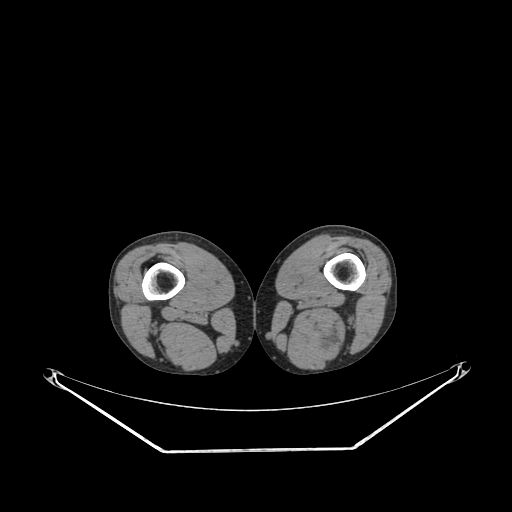
CT of an extremity soft-tissue mass (from a PET/CT study), one axial slice. Slice 203 of 267 in the series (ordered by position). 140 kVp. Soft-tissue window (W 400 / L 40 HU). 3.75 mm slice thickness. 512 × 512 image matrix, field of view 500 × 500 mm. Male patient. From the clinical record (not read from this slice): histological type: synovial sarcoma; site of the primary tumour: left poplietal fossa.
Outlined on this slice (expert contour drawn on MRI and transferred to this co-registered scan by the dataset authors):
- gross tumour volume (mass): bounding box [x1, y1, x2, y2] px = [315, 335, 325, 350]